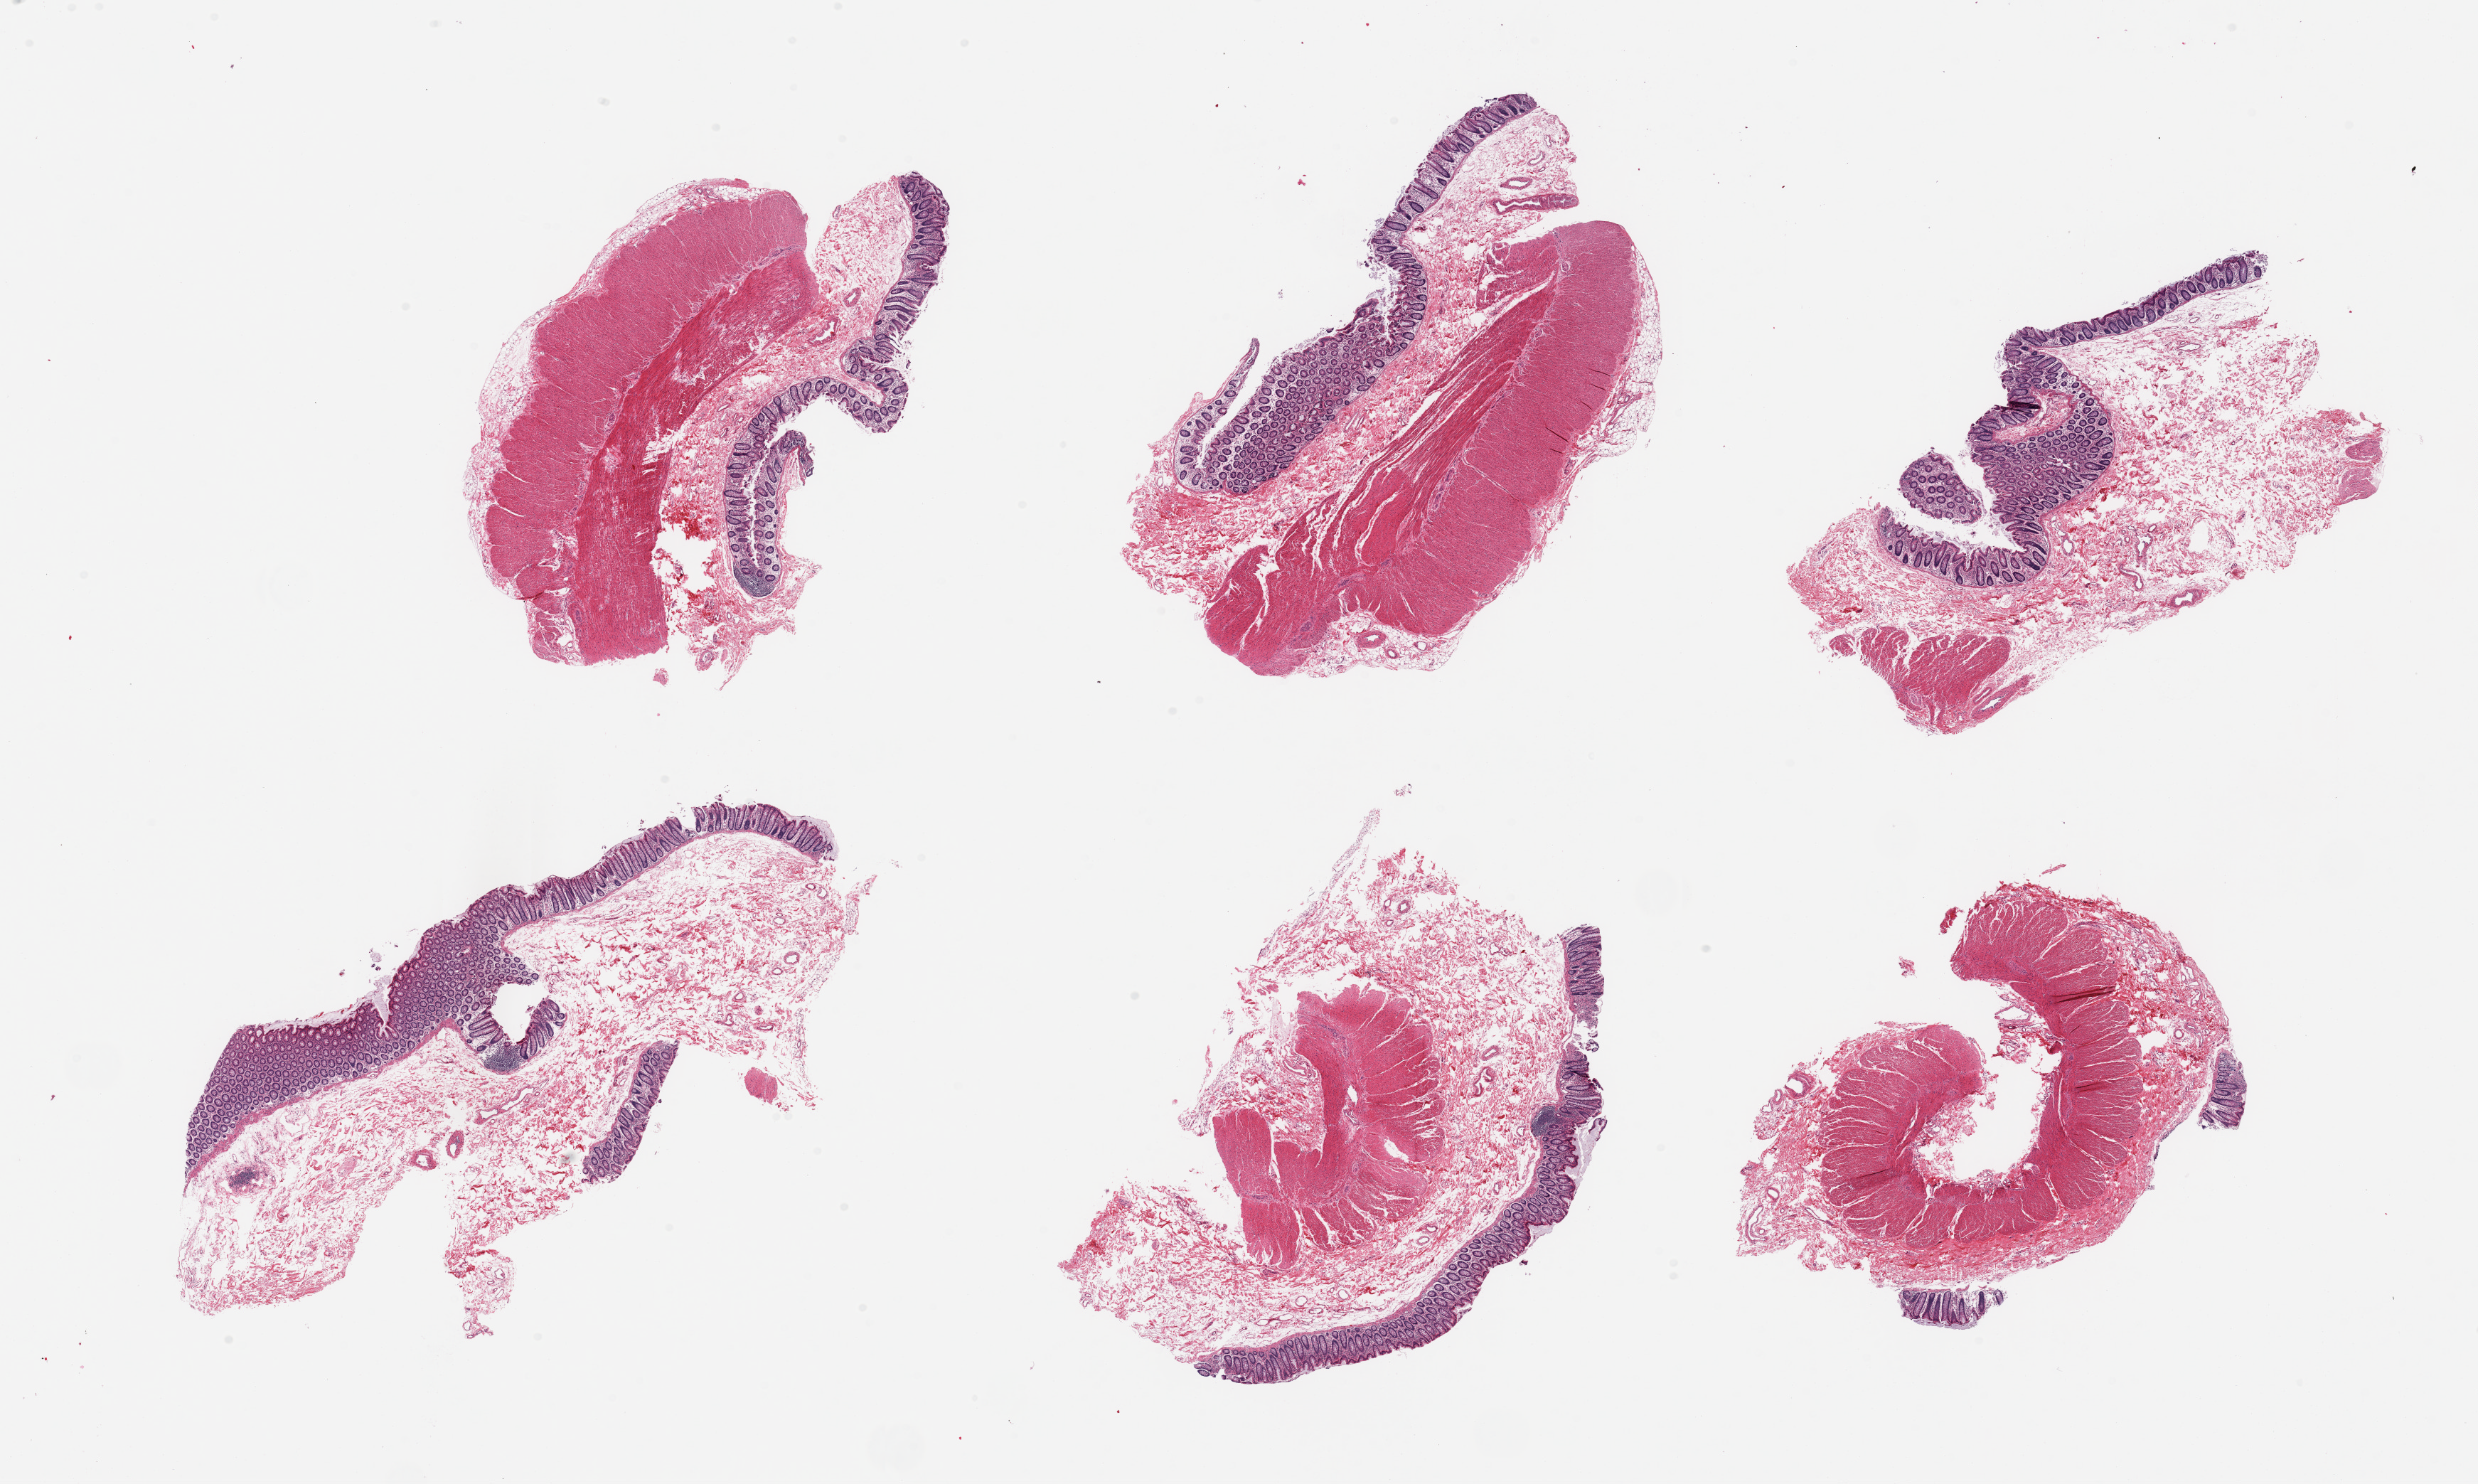
Whole-slide image, H&E stain, brightfield, low-resolution overview of the scanned area, about 27.6 x 16.5 mm. PAXgene-fixed paraffin-embedded (PFPE) section. Sampled site (target tissue): transverse colon. Tissue donor sample.
• pathologist's review note for this sample: 6 pieces; variable composition of mucosa, submucosa, muscularis